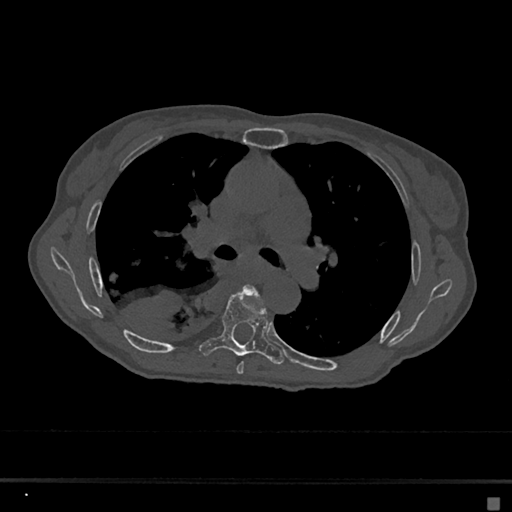
CT including the spine, one axial slice. Slice 428 of 797 in the series (ordered by position). Reconstruction kernel Br40s/3. 120 kVp. Bone window (W 1800 / L 400 HU). 0.5 mm slice thickness. 512 × 512 image matrix, field of view 360 × 360 mm. Patient: female, 68 years. From the clinical record (not read from this slice): primary cancer: renal.
Structures marked on this image (semi-automatic segmentation, software-assisted and operator-edited):
- T5 vertebra: box from (x=236, y=285) to (x=261, y=375) px
- T6 vertebra: (x=200, y=289)–(x=284, y=365)